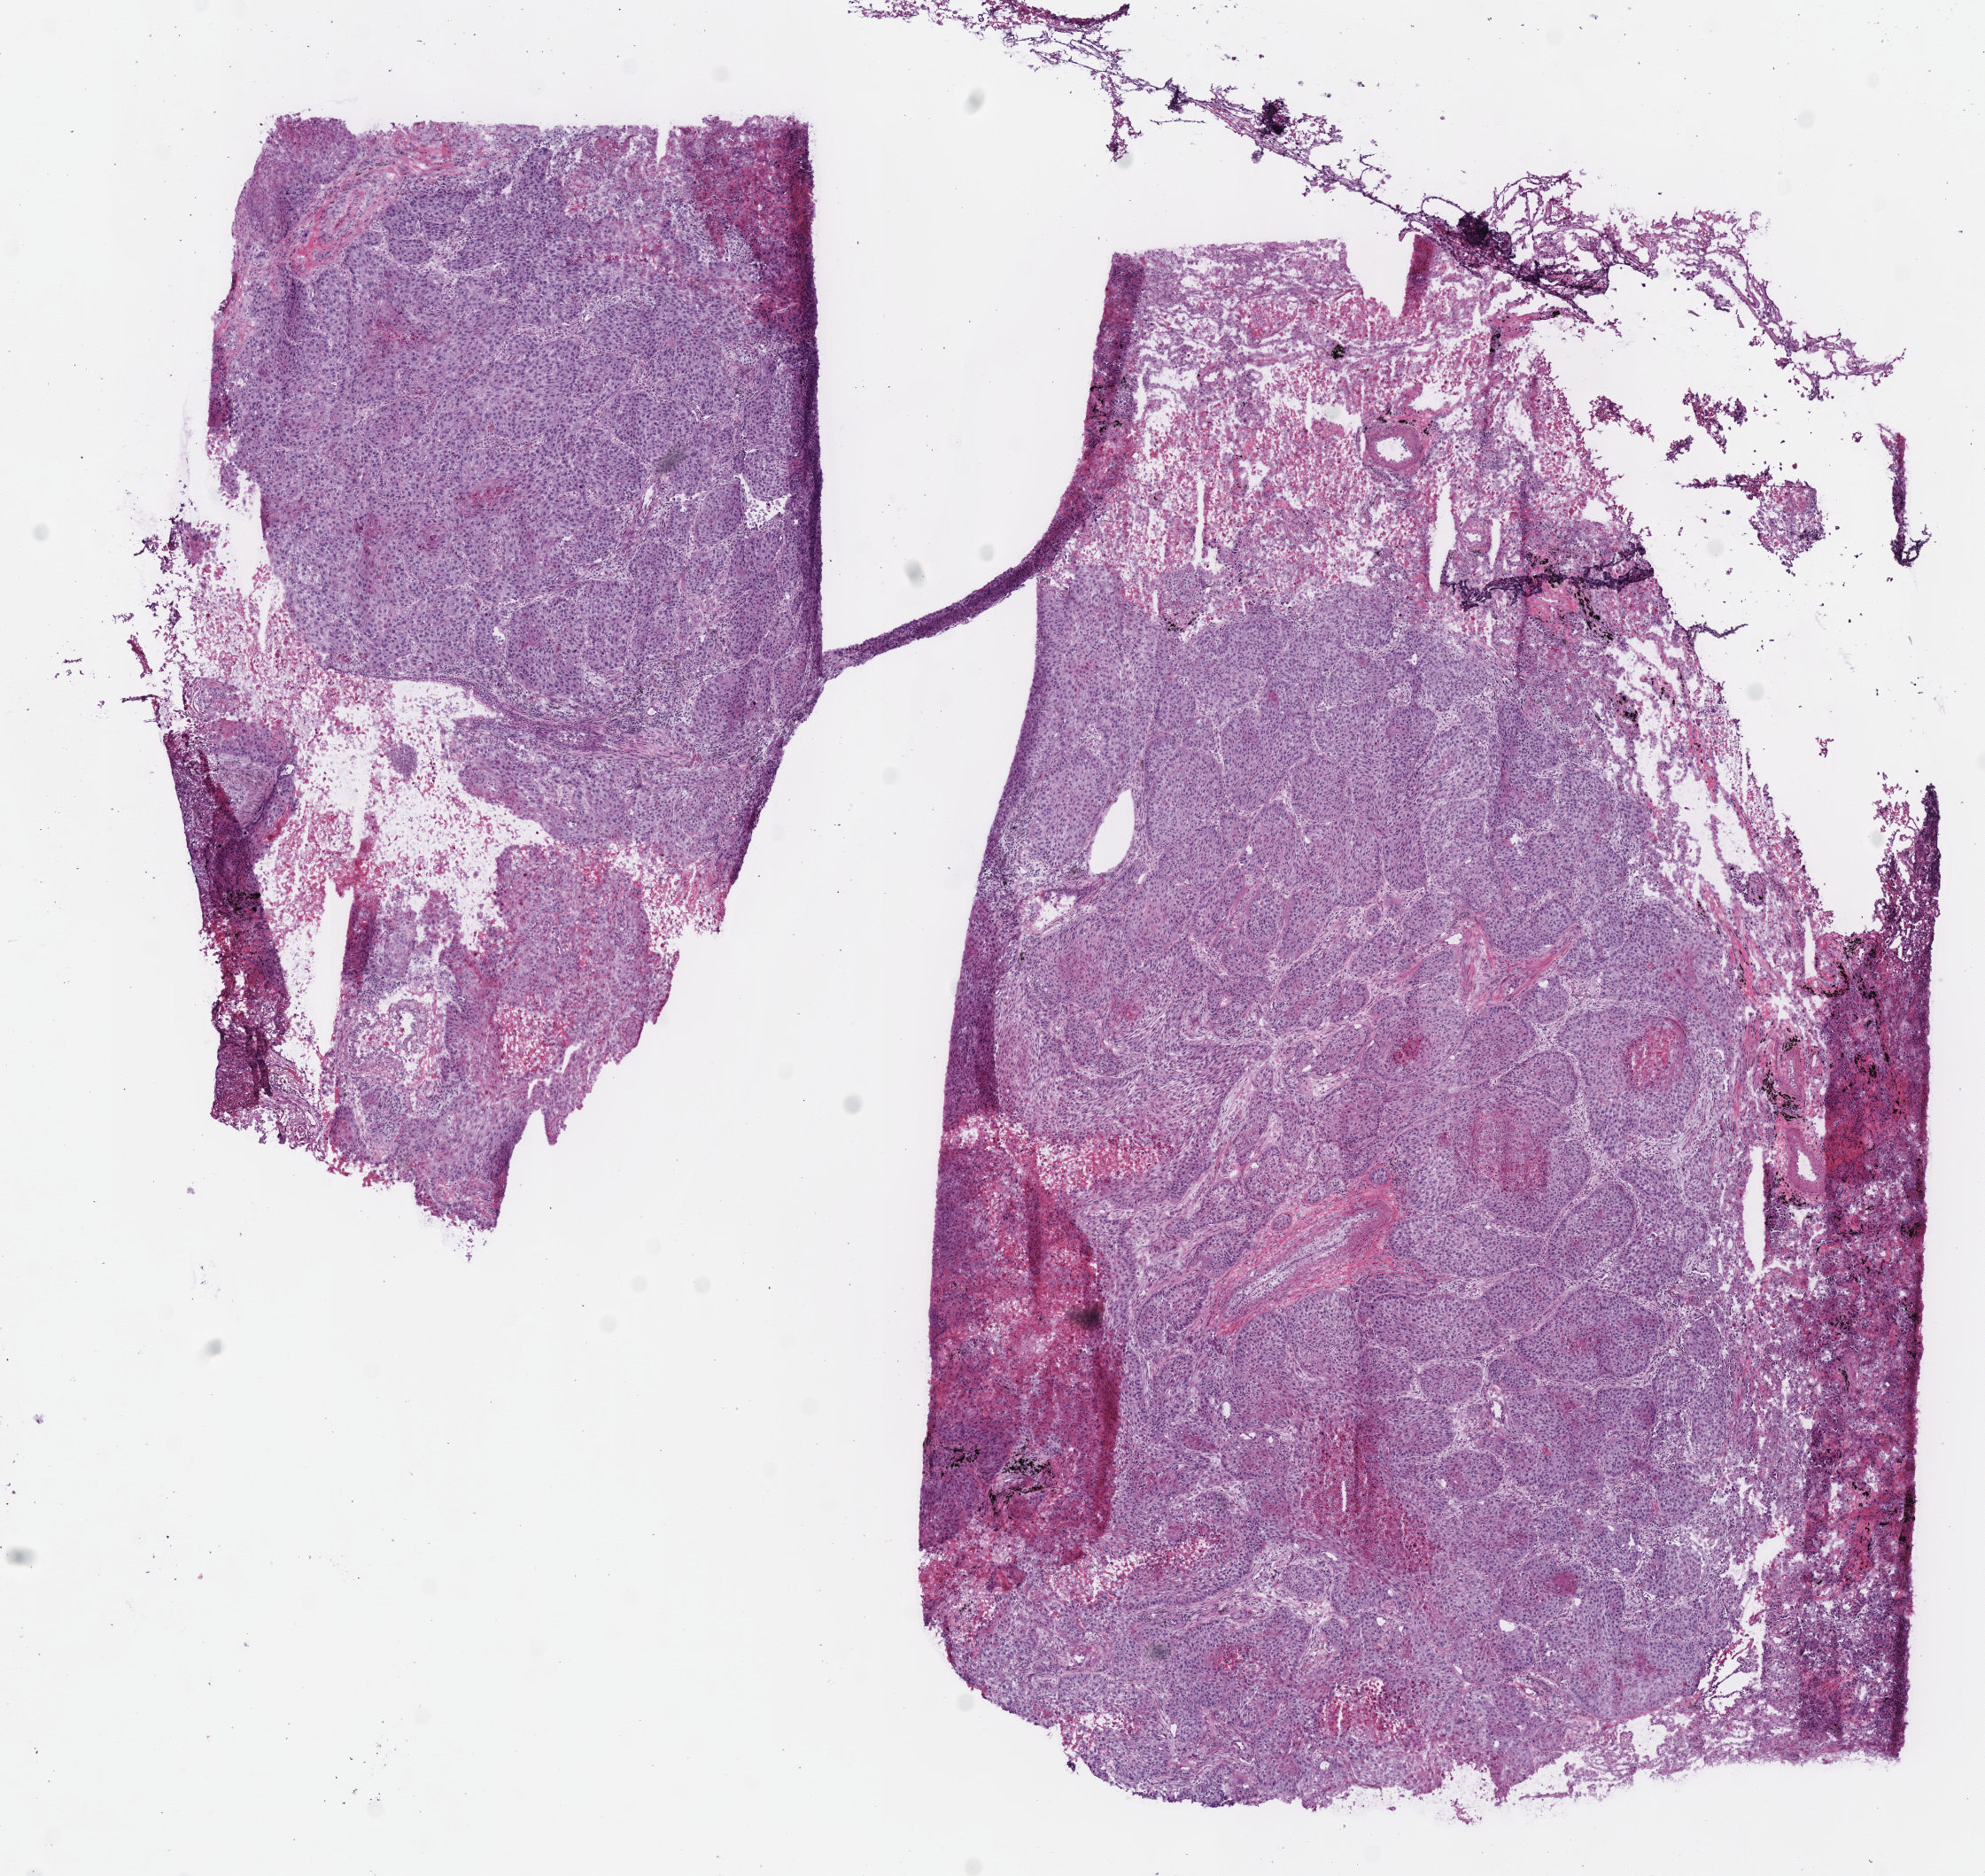
H&E whole-slide image — a low-resolution overview of the entire scanned area, about 8.8 x 8.3 mm (acquisition: 40x scan). Frozen section from the bottom of the tissue portion. Lung, primary tumour sample. Male patient; age at initial diagnosis 75 years. Slide review estimates, as recorded: tumour cells 75%, tumour nuclei 80%, normal cells 17%, stromal cells 0%, necrosis 8%. Infiltration values recorded for this section: lymphocyte infiltration 5%, monocyte infiltration 5%.
* TNM: T3 NX M1
* histologic diagnosis: Squamous cell carcinoma, NOS (upper lobe, lung)
* AJCC pathologic stage: IV (6th edition)